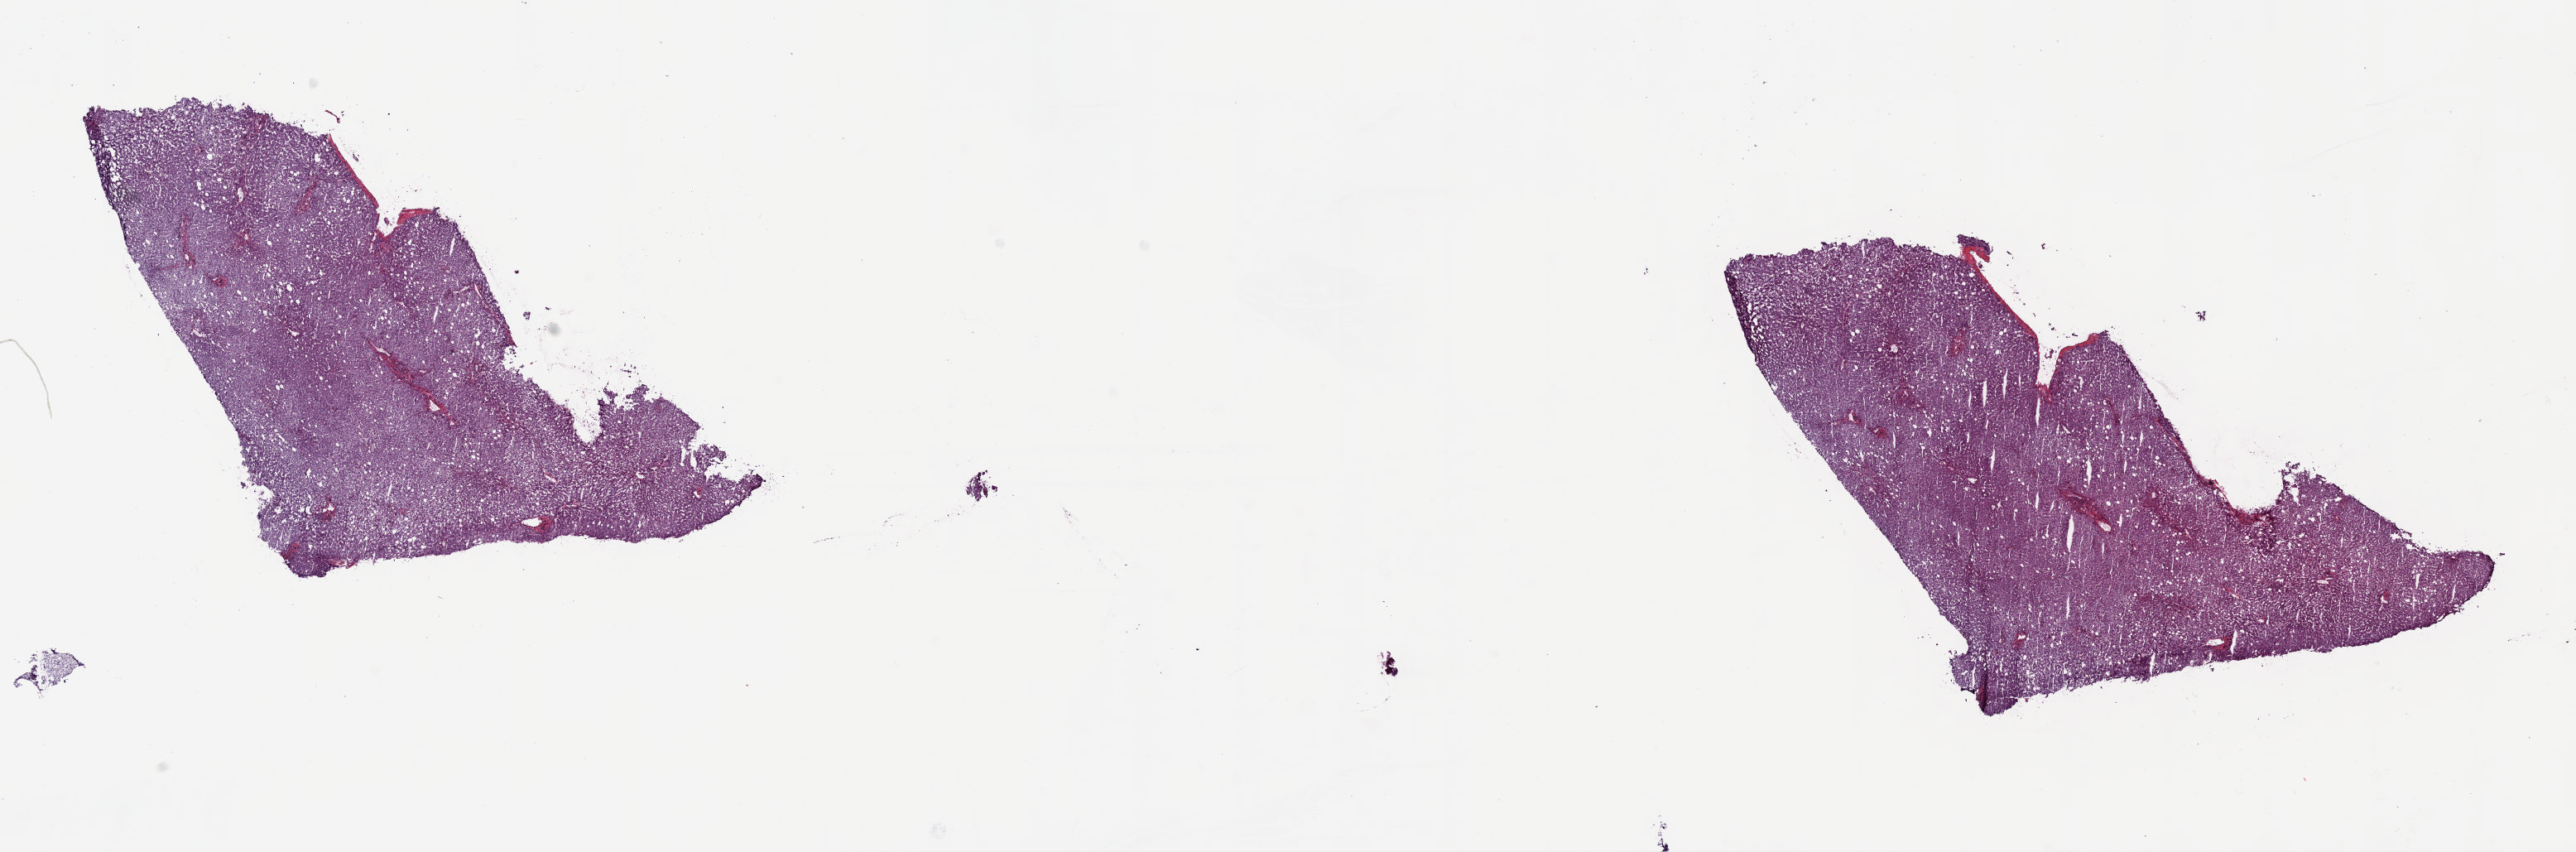
Digitized H&E-stained tissue section (whole slide) — shown as a low-resolution overview of the whole scanned area (about 24.5 x 8.1 mm). Frozen section from the top of the tissue portion. Solid tissue normal (non-tumour tissue) sample from the liver. Female, age 54 years at initial diagnosis. Slide review estimates, as recorded: tumour cells 0%, tumour nuclei 0%, normal cells 100%, stromal cells 0%, necrosis 0%. Inflammatory infiltration, as recorded: lymphocyte infiltration 6%, monocyte infiltration 1%, neutrophil infiltration 6%.
This section: solid tissue normal sample (biorepository sample class). Patient diagnosis: Hepatocellular carcinoma, NOS.